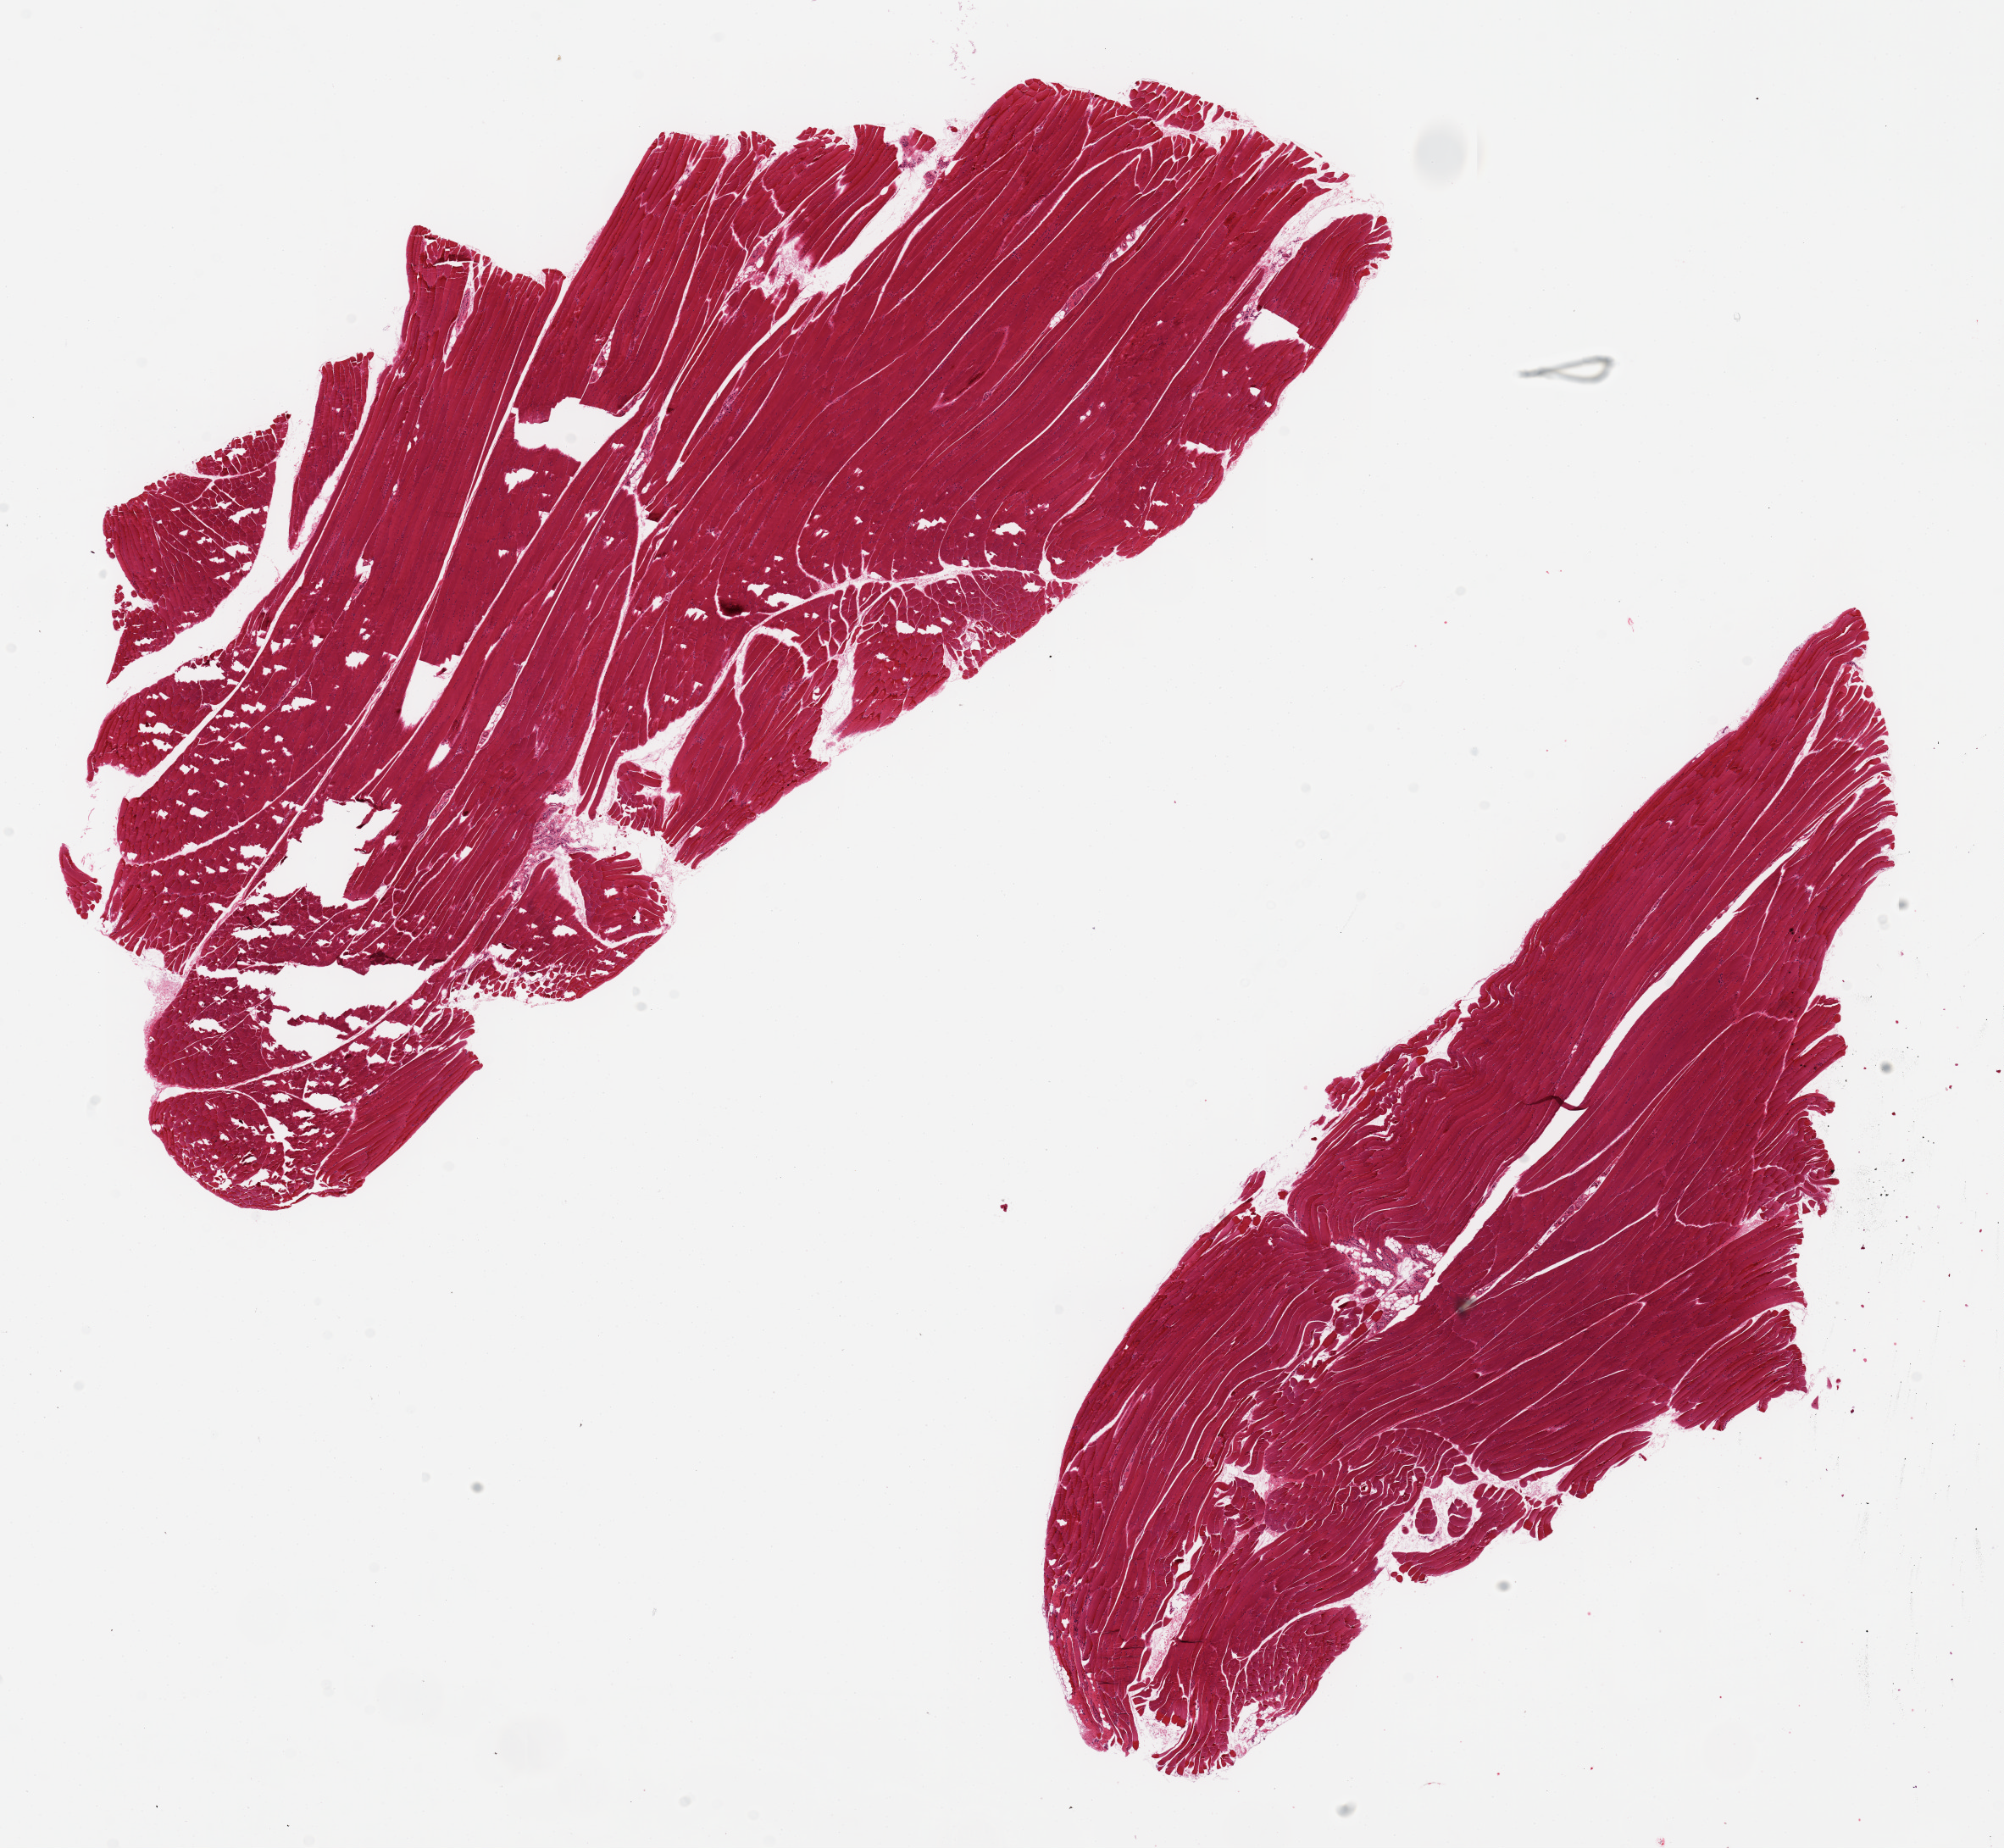
Haematoxylin and eosin whole-slide image — low-resolution overview of the scanned area, about 18.7 x 17.2 mm, PAXgene-fixed paraffin-embedded (PFPE) section, section of skeletal muscle (target tissue), donor tissue sample. Donor: female.
Review note (as recorded): 2 pieces, one 14 x 6mm with moderate fragmentation.